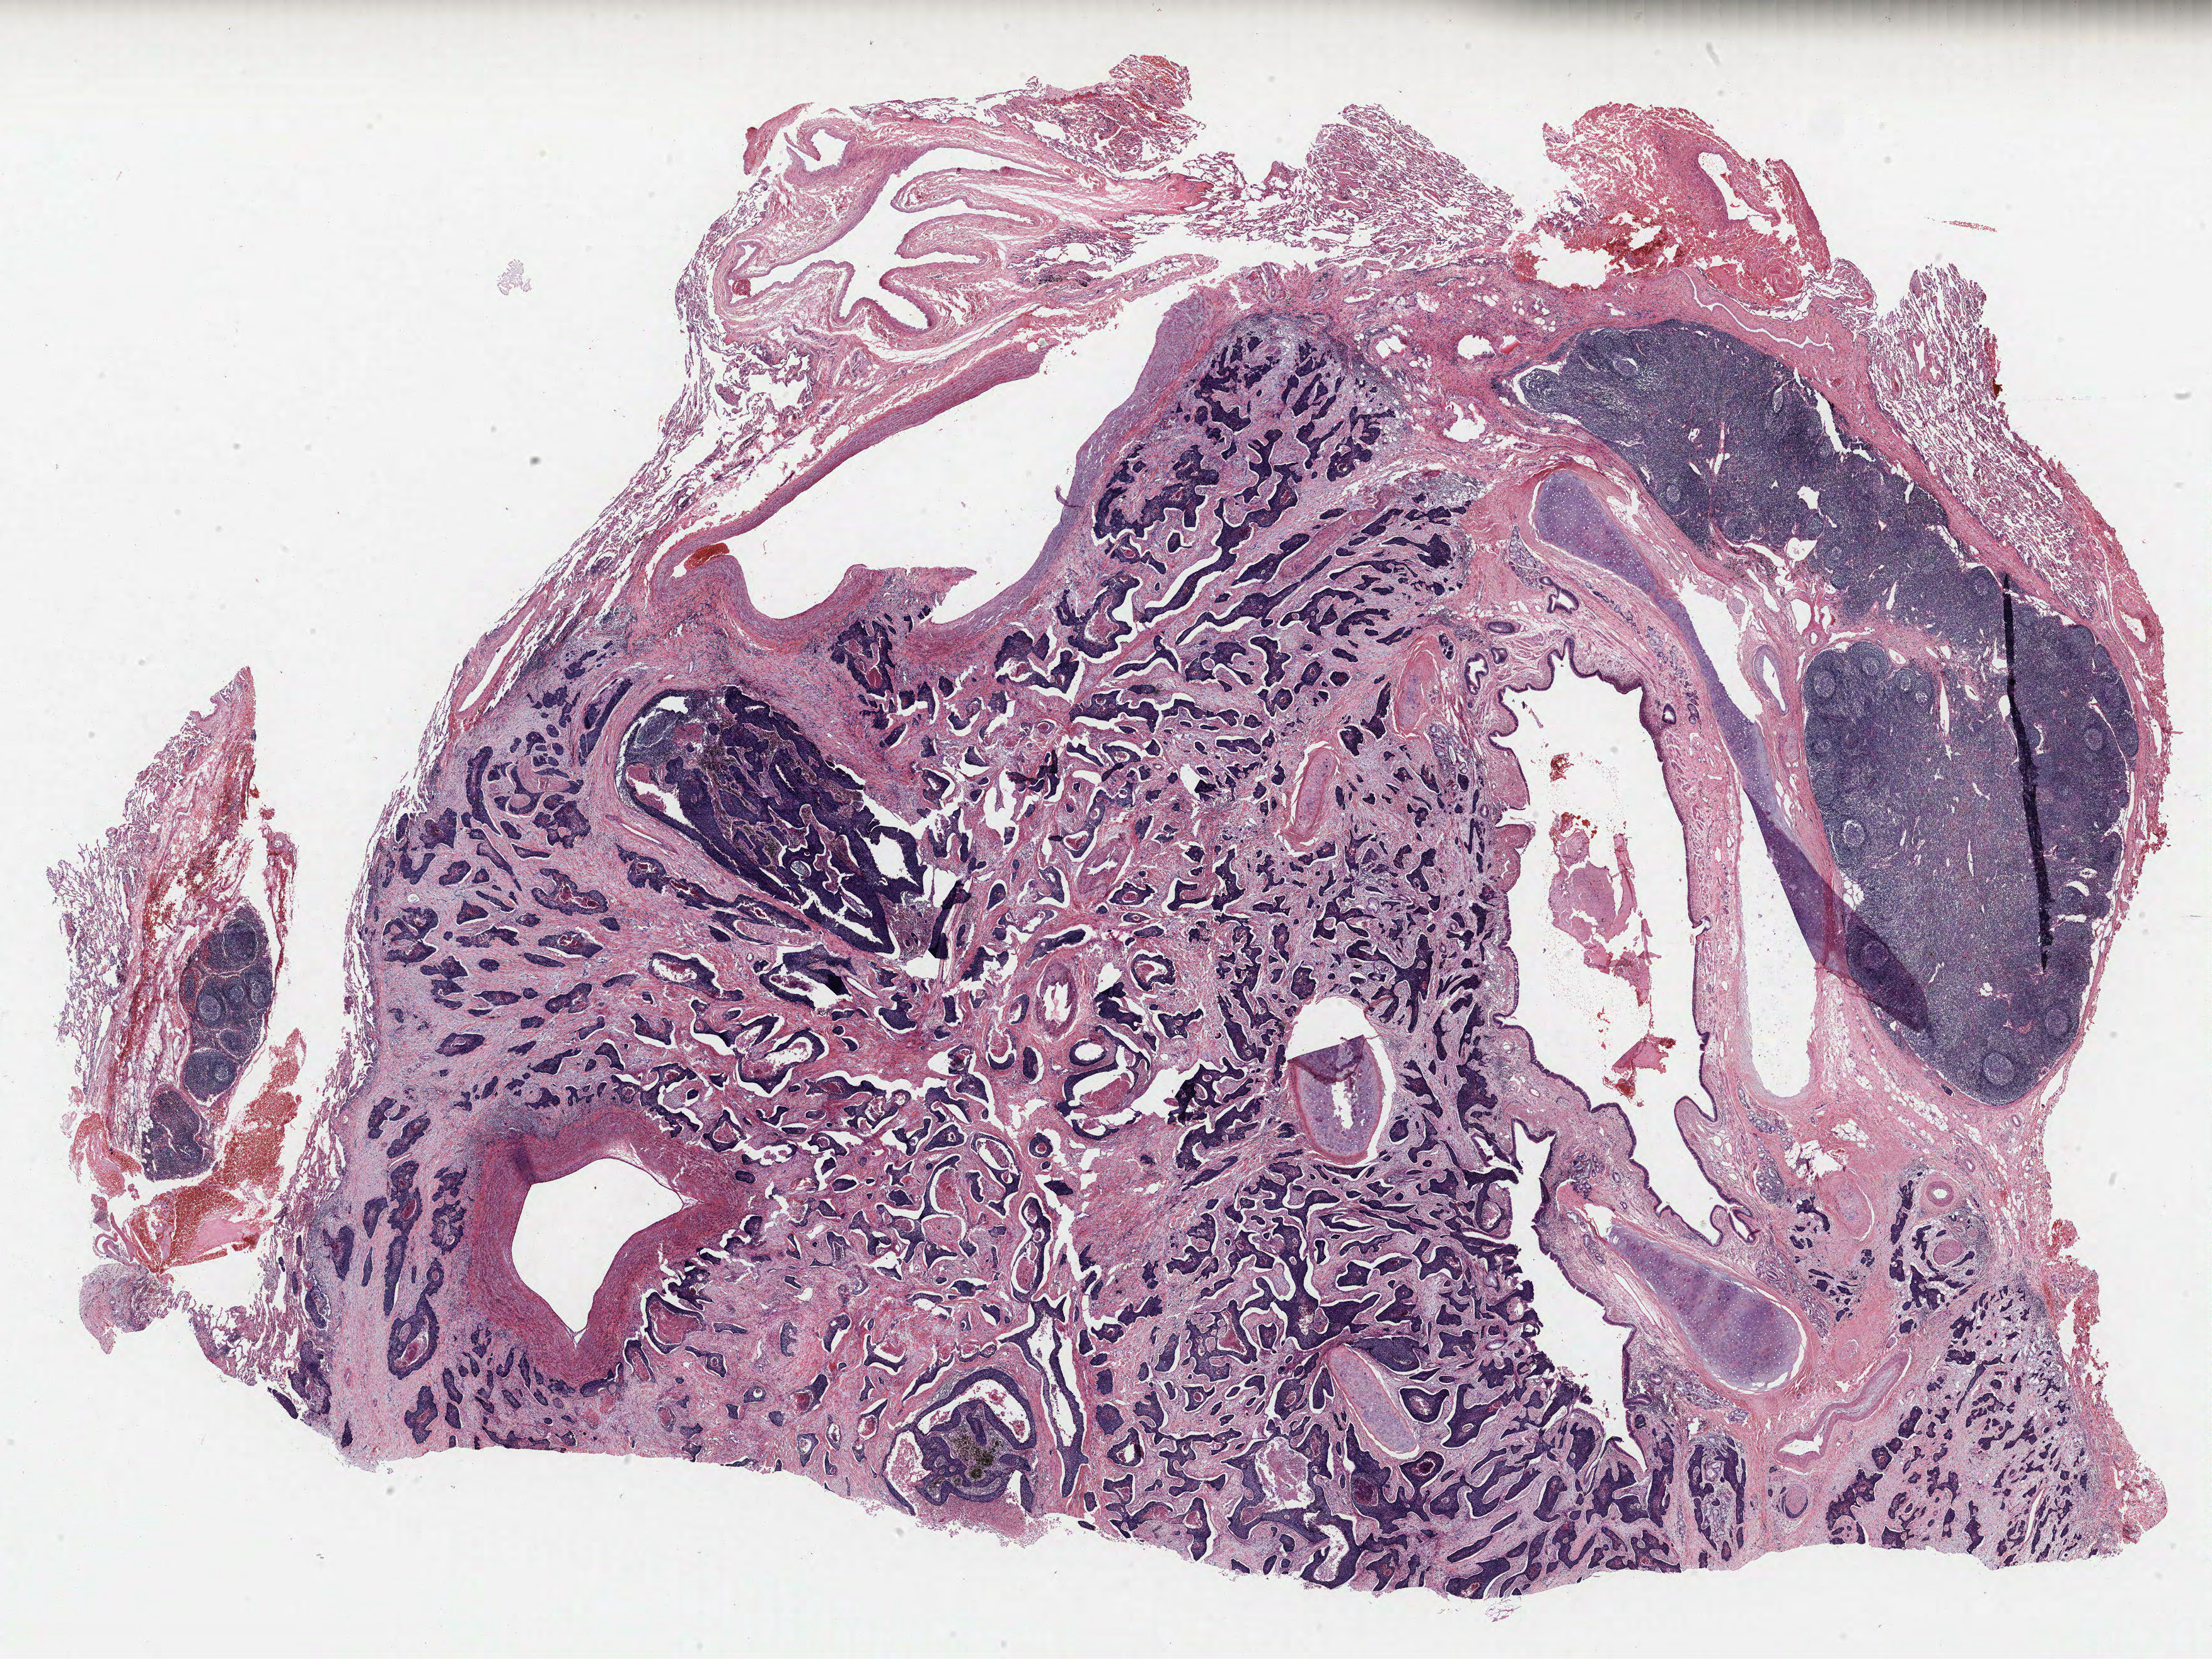
H&E-stained whole-slide image, low-resolution overview of the scanned area, about 28.1 x 21.1 mm; formalin-fixed paraffin-embedded (FFPE) section; lung. Female, age 57 at enrolment. Current smoker at enrolment. Grade: moderately differentiated (G2).
- stage (AJCC 6th edition): IIB
- participant's lung-cancer diagnosis: Basaloid squamous cell carcinoma
- tumour size (pathology): 32 mm
- primary tumour location (clinical record): left lower lobe